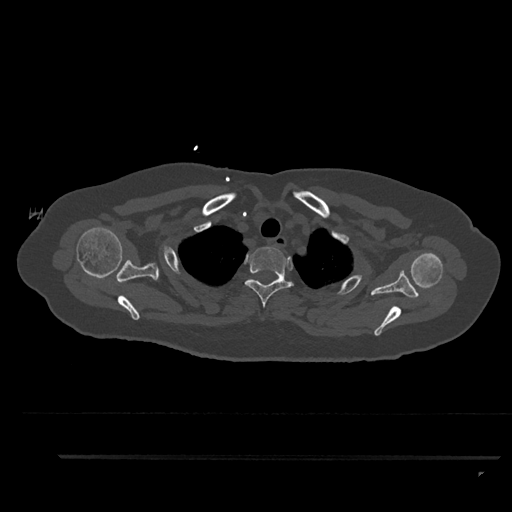
CT including the spine, one axial slice; reconstruction kernel Br40s/3; bone window (W 1800 / L 400 HU); 0.5 mm slice thickness; 512 × 512 image matrix. Female patient, age 44 years. From the clinical record (not read from this slice): primary cancer: renal; vertebrae with lytic lesions (as recorded): L1.
Outlined on this slice (semi-automatic segmentation, software-assisted and operator-edited):
- T2 vertebra: bounding box [x1, y1, x2, y2] px = [244, 247, 294, 308]